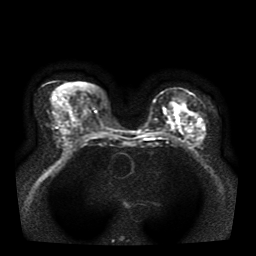
Breast MRI, one axial slice. Diffusion-weighted series; image 2 of 4 stored at this slice position (different b-values; order by instance number). 1.5 T. 5 mm slice thickness. 256 × 256 image matrix. Female patient.
Outlined on this slice (outlined manually by an expert reader):
- tumour on diffusion-weighted imaging: bounding box (x1, y1, x2, y2) in pixels: (175, 103, 186, 114)